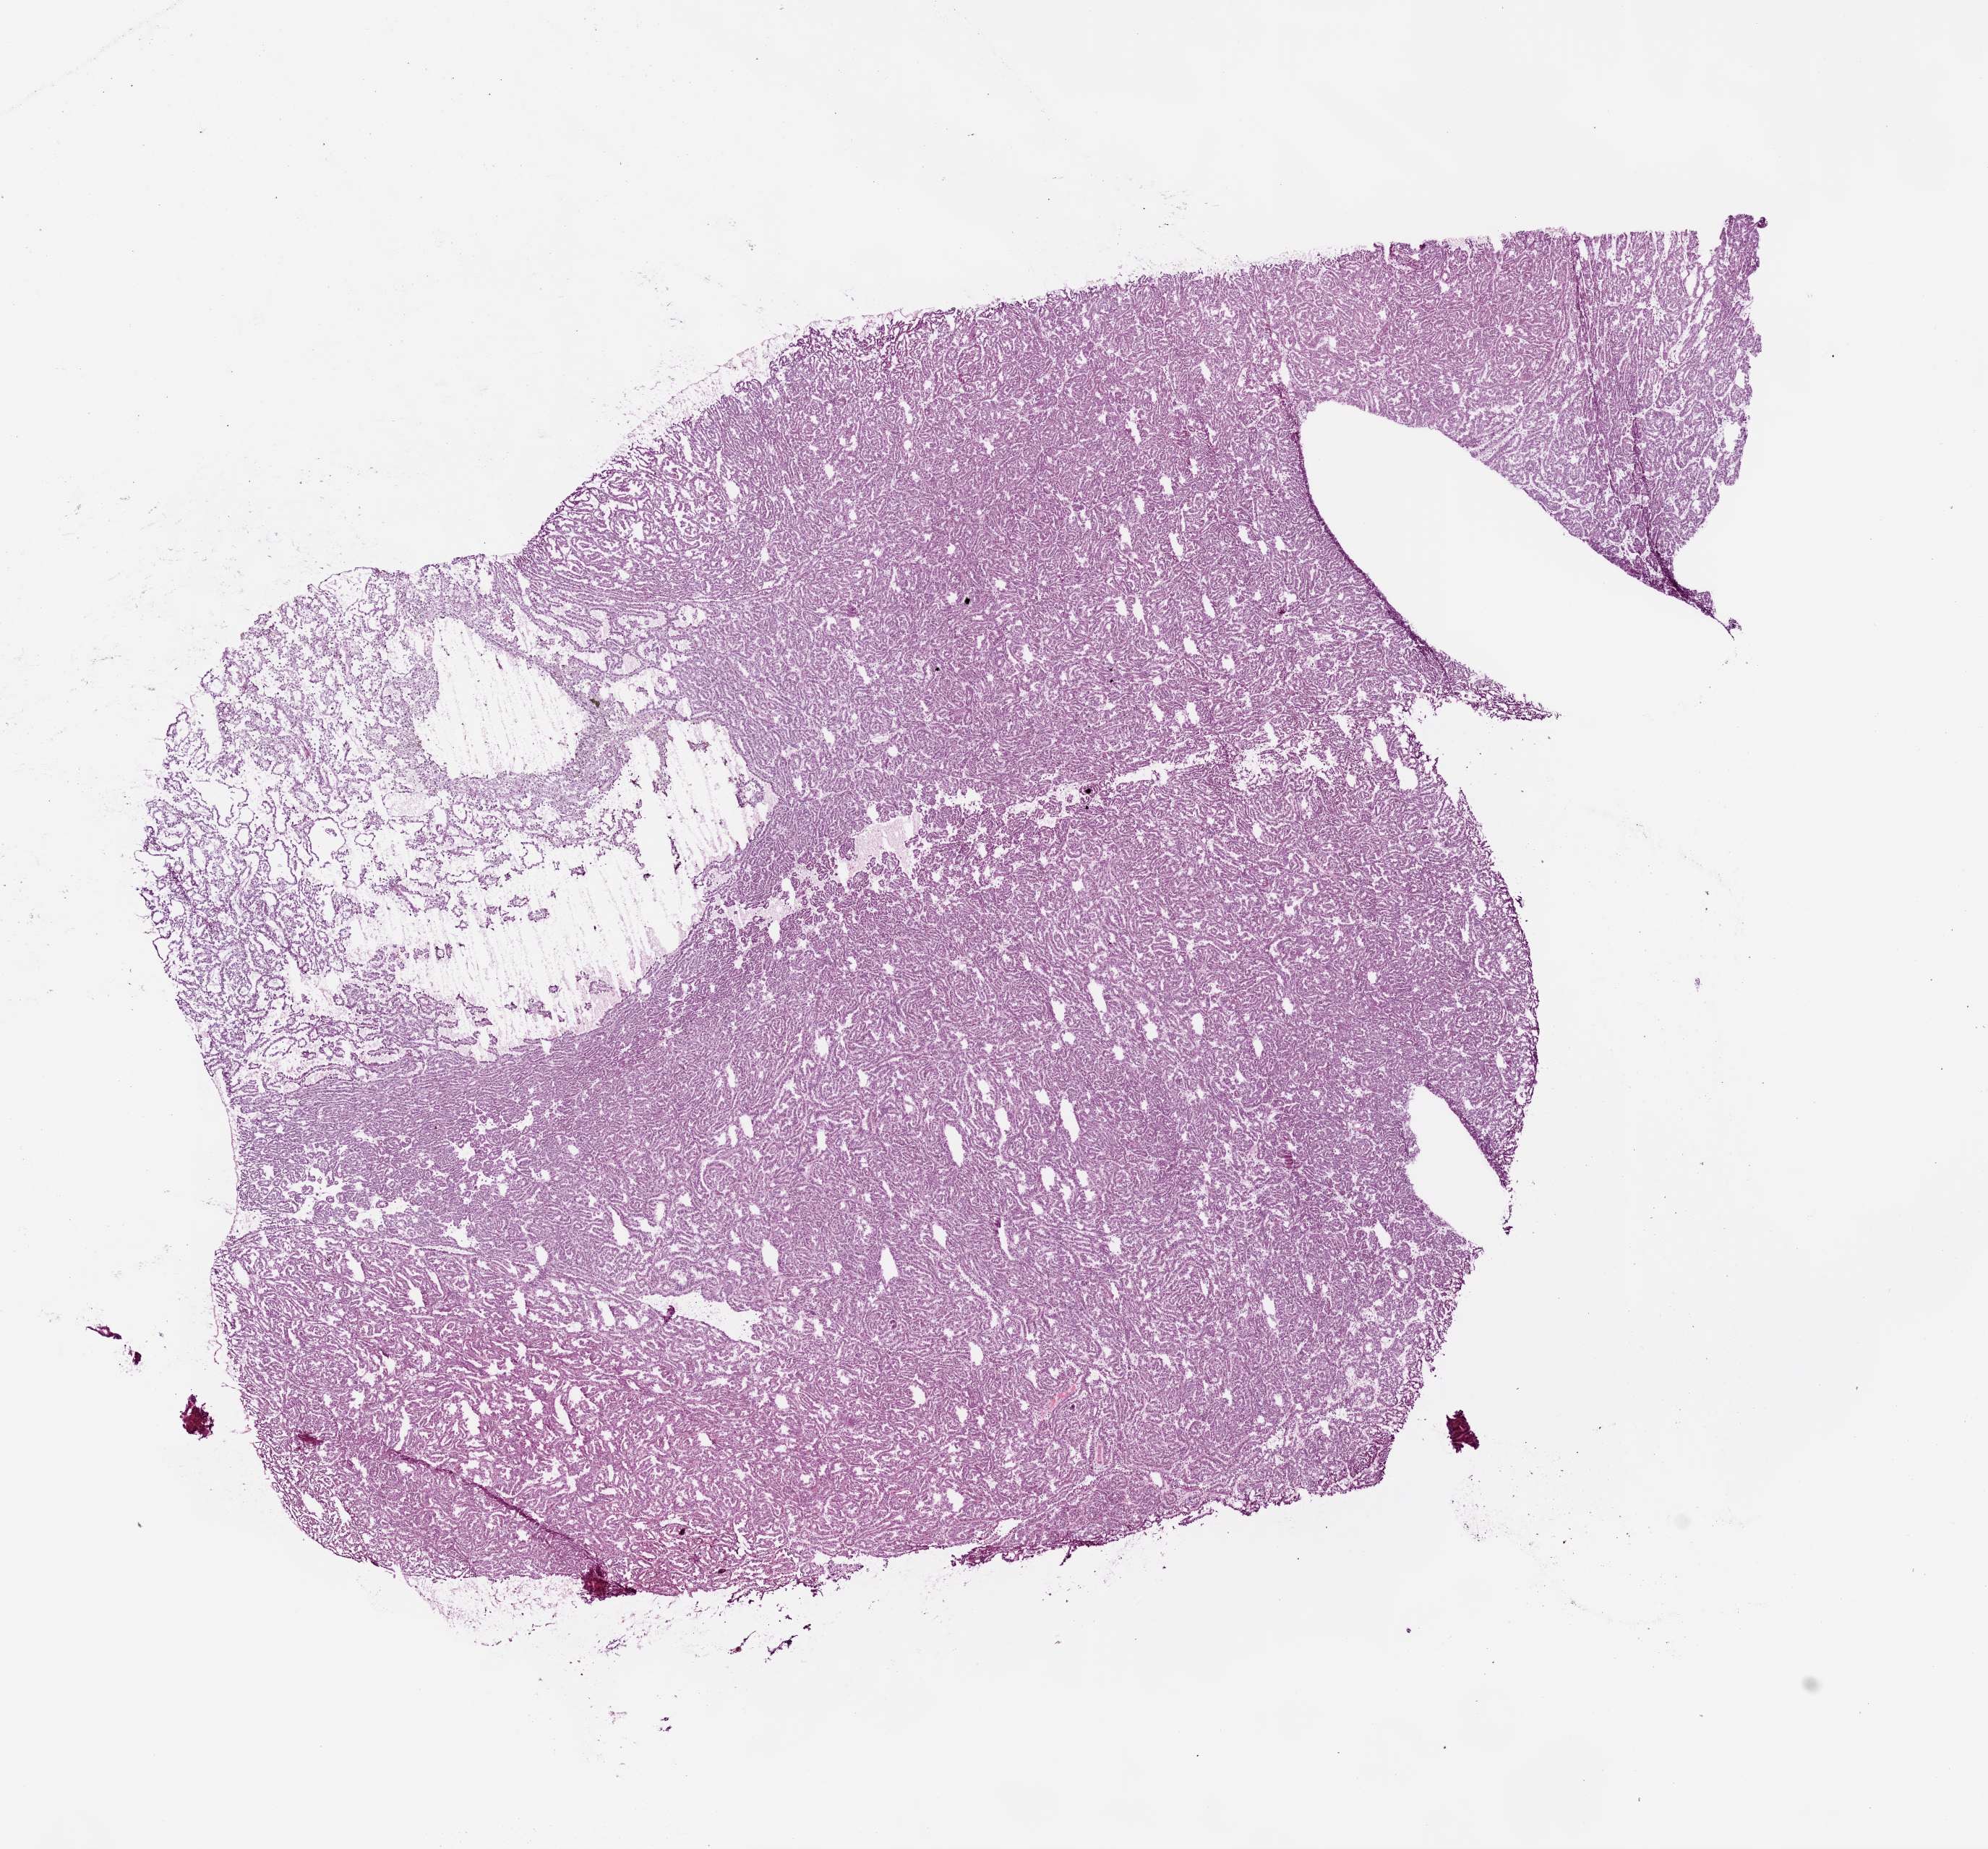
Whole-slide histology image, H&E, whole scanned area (about 11.0 x 10.3 mm, slide scanned at 20x) shown as a low-resolution overview. Frozen section from the bottom of the tissue portion. Primary tumour sample from the kidney. Male patient; age at initial diagnosis 71 years. Pathologist review of this section (percent, as recorded): tumour cells 95%, tumour nuclei 90%, normal cells 0%, stromal cells 5%, necrosis 0%.
AJCC pathologic stage: III. Laterality: right. TNM: T3a NX. Histologic diagnosis: Papillary adenocarcinoma, NOS.